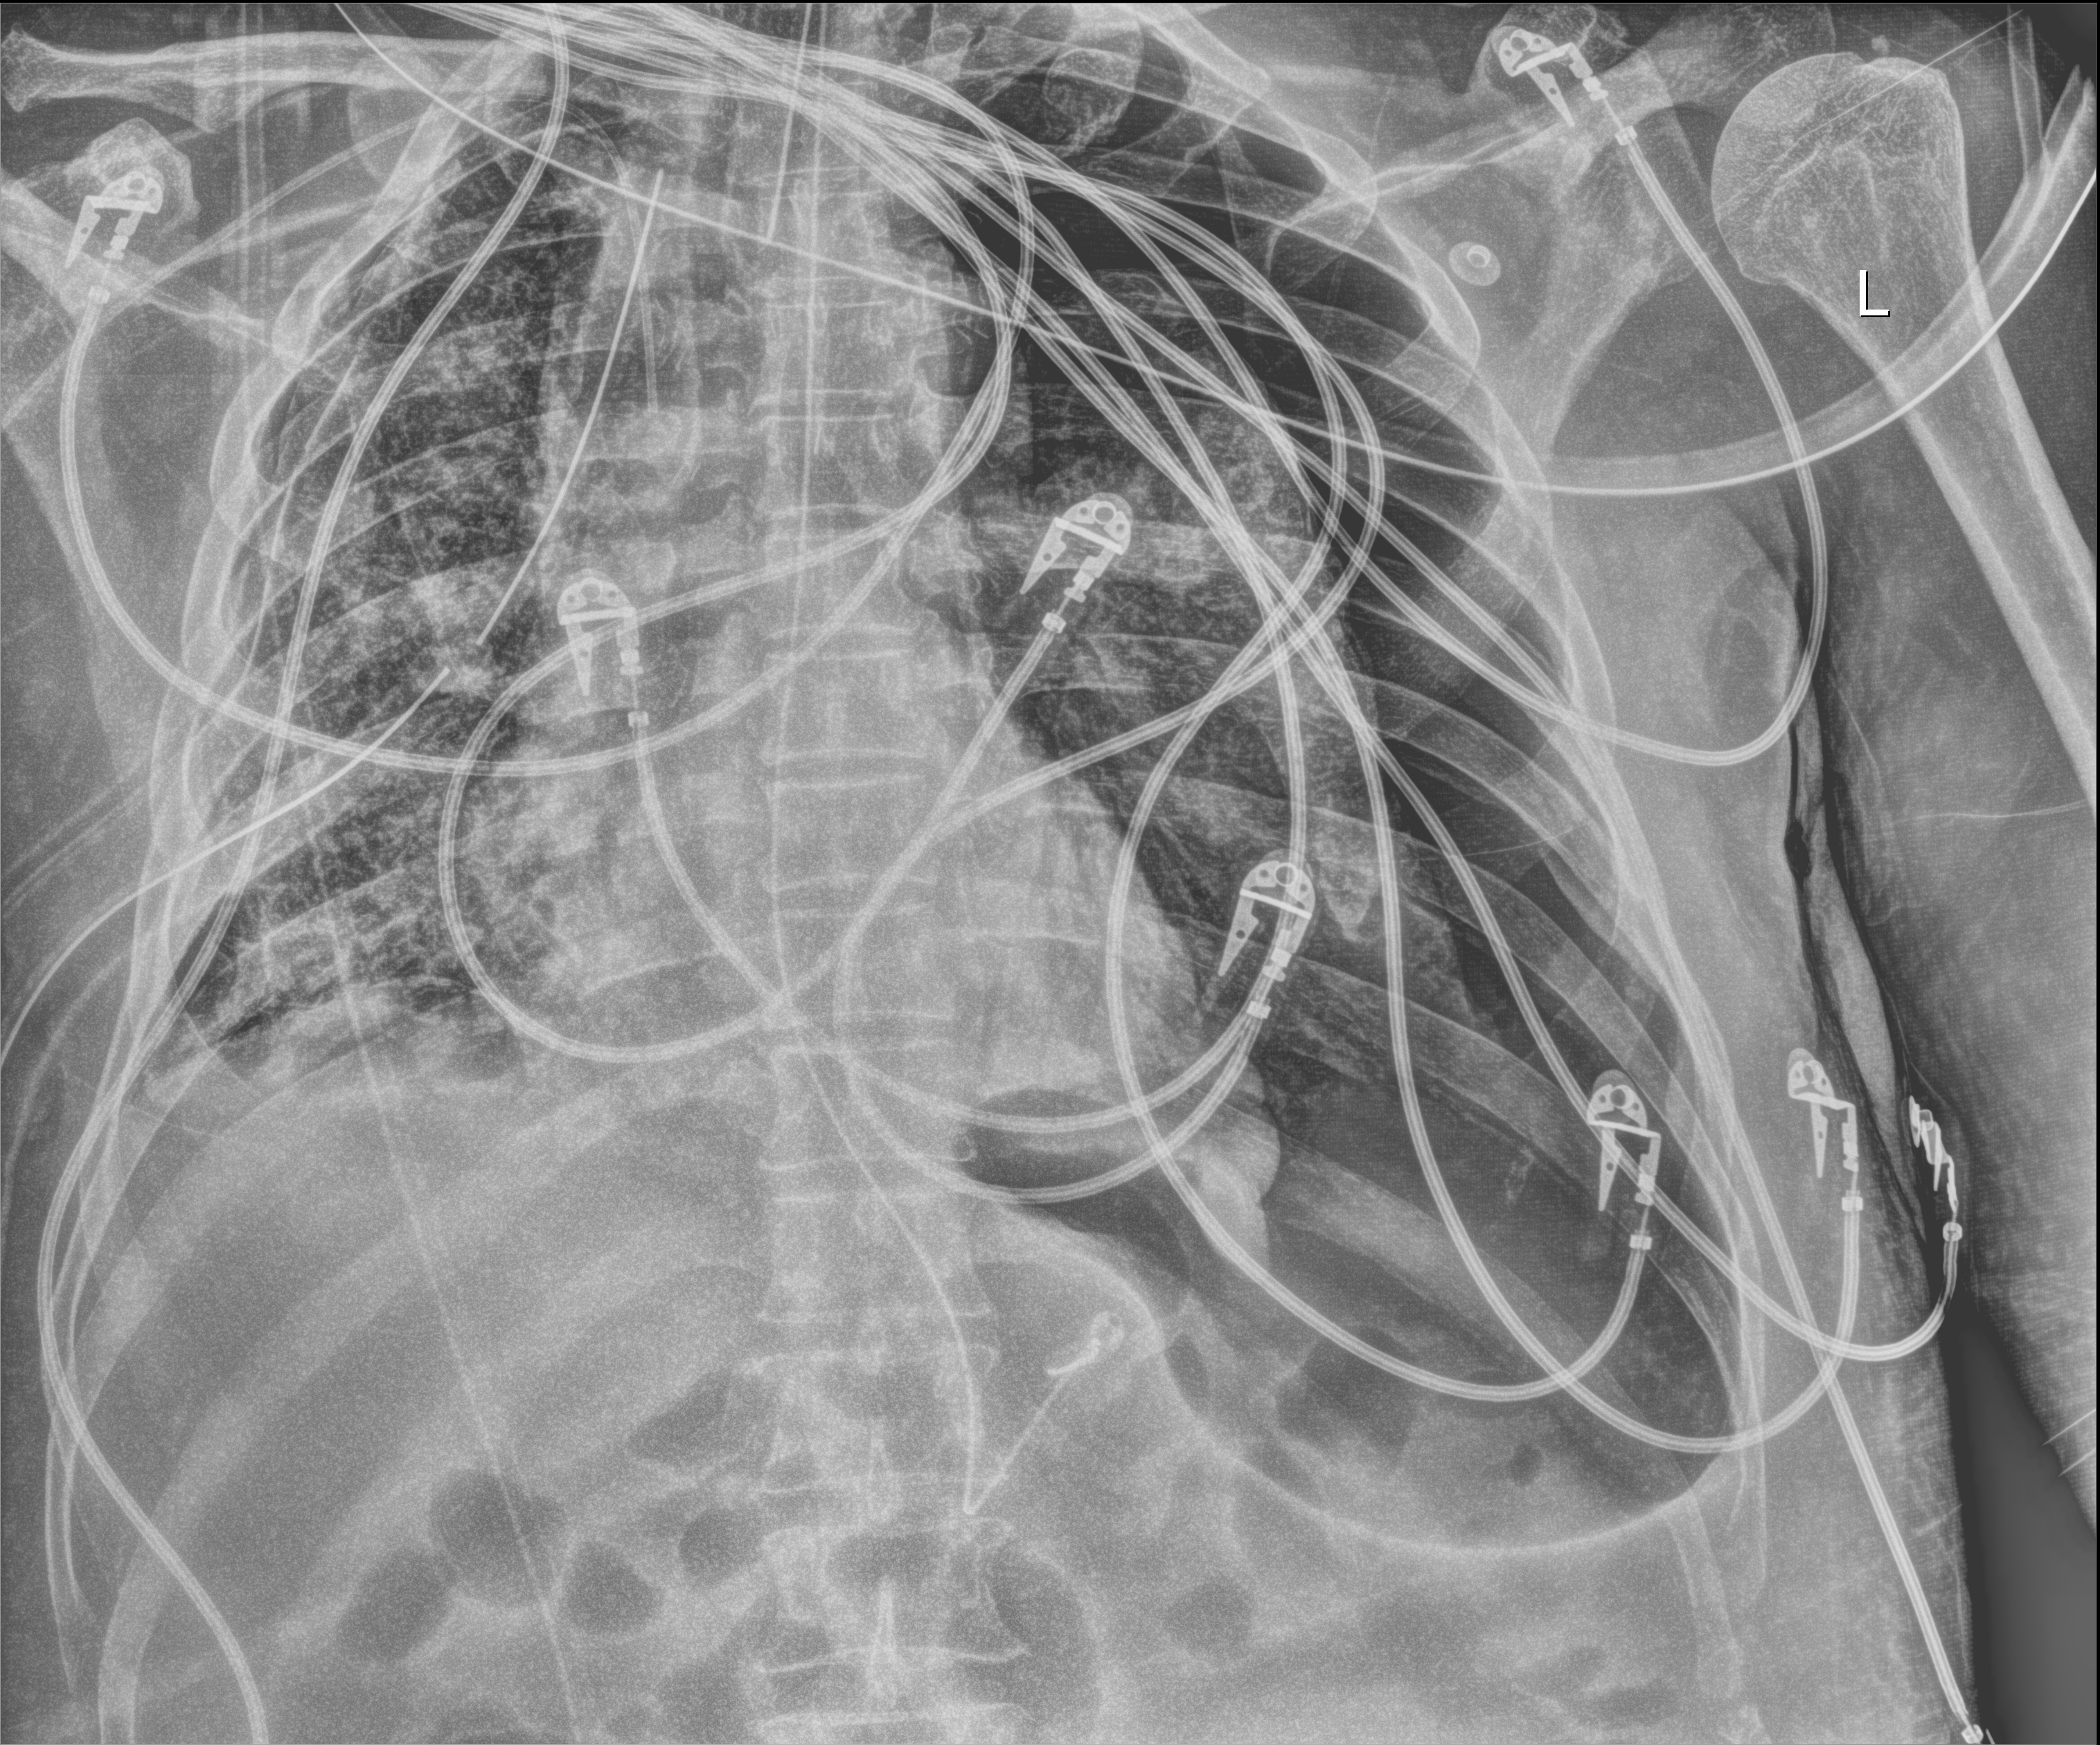
Chest X-ray (portable); anteroposterior (AP) projection. Male patient hospitalised with COVID-19, age 60–74 years.
Hospital-stay facts (about this admission, not read from this image; timing relative to this image not recorded):
- chronic kidney disease (admission record): no
- smoking status (admission record): never
- admitted to intensive care during this hospital stay: yes